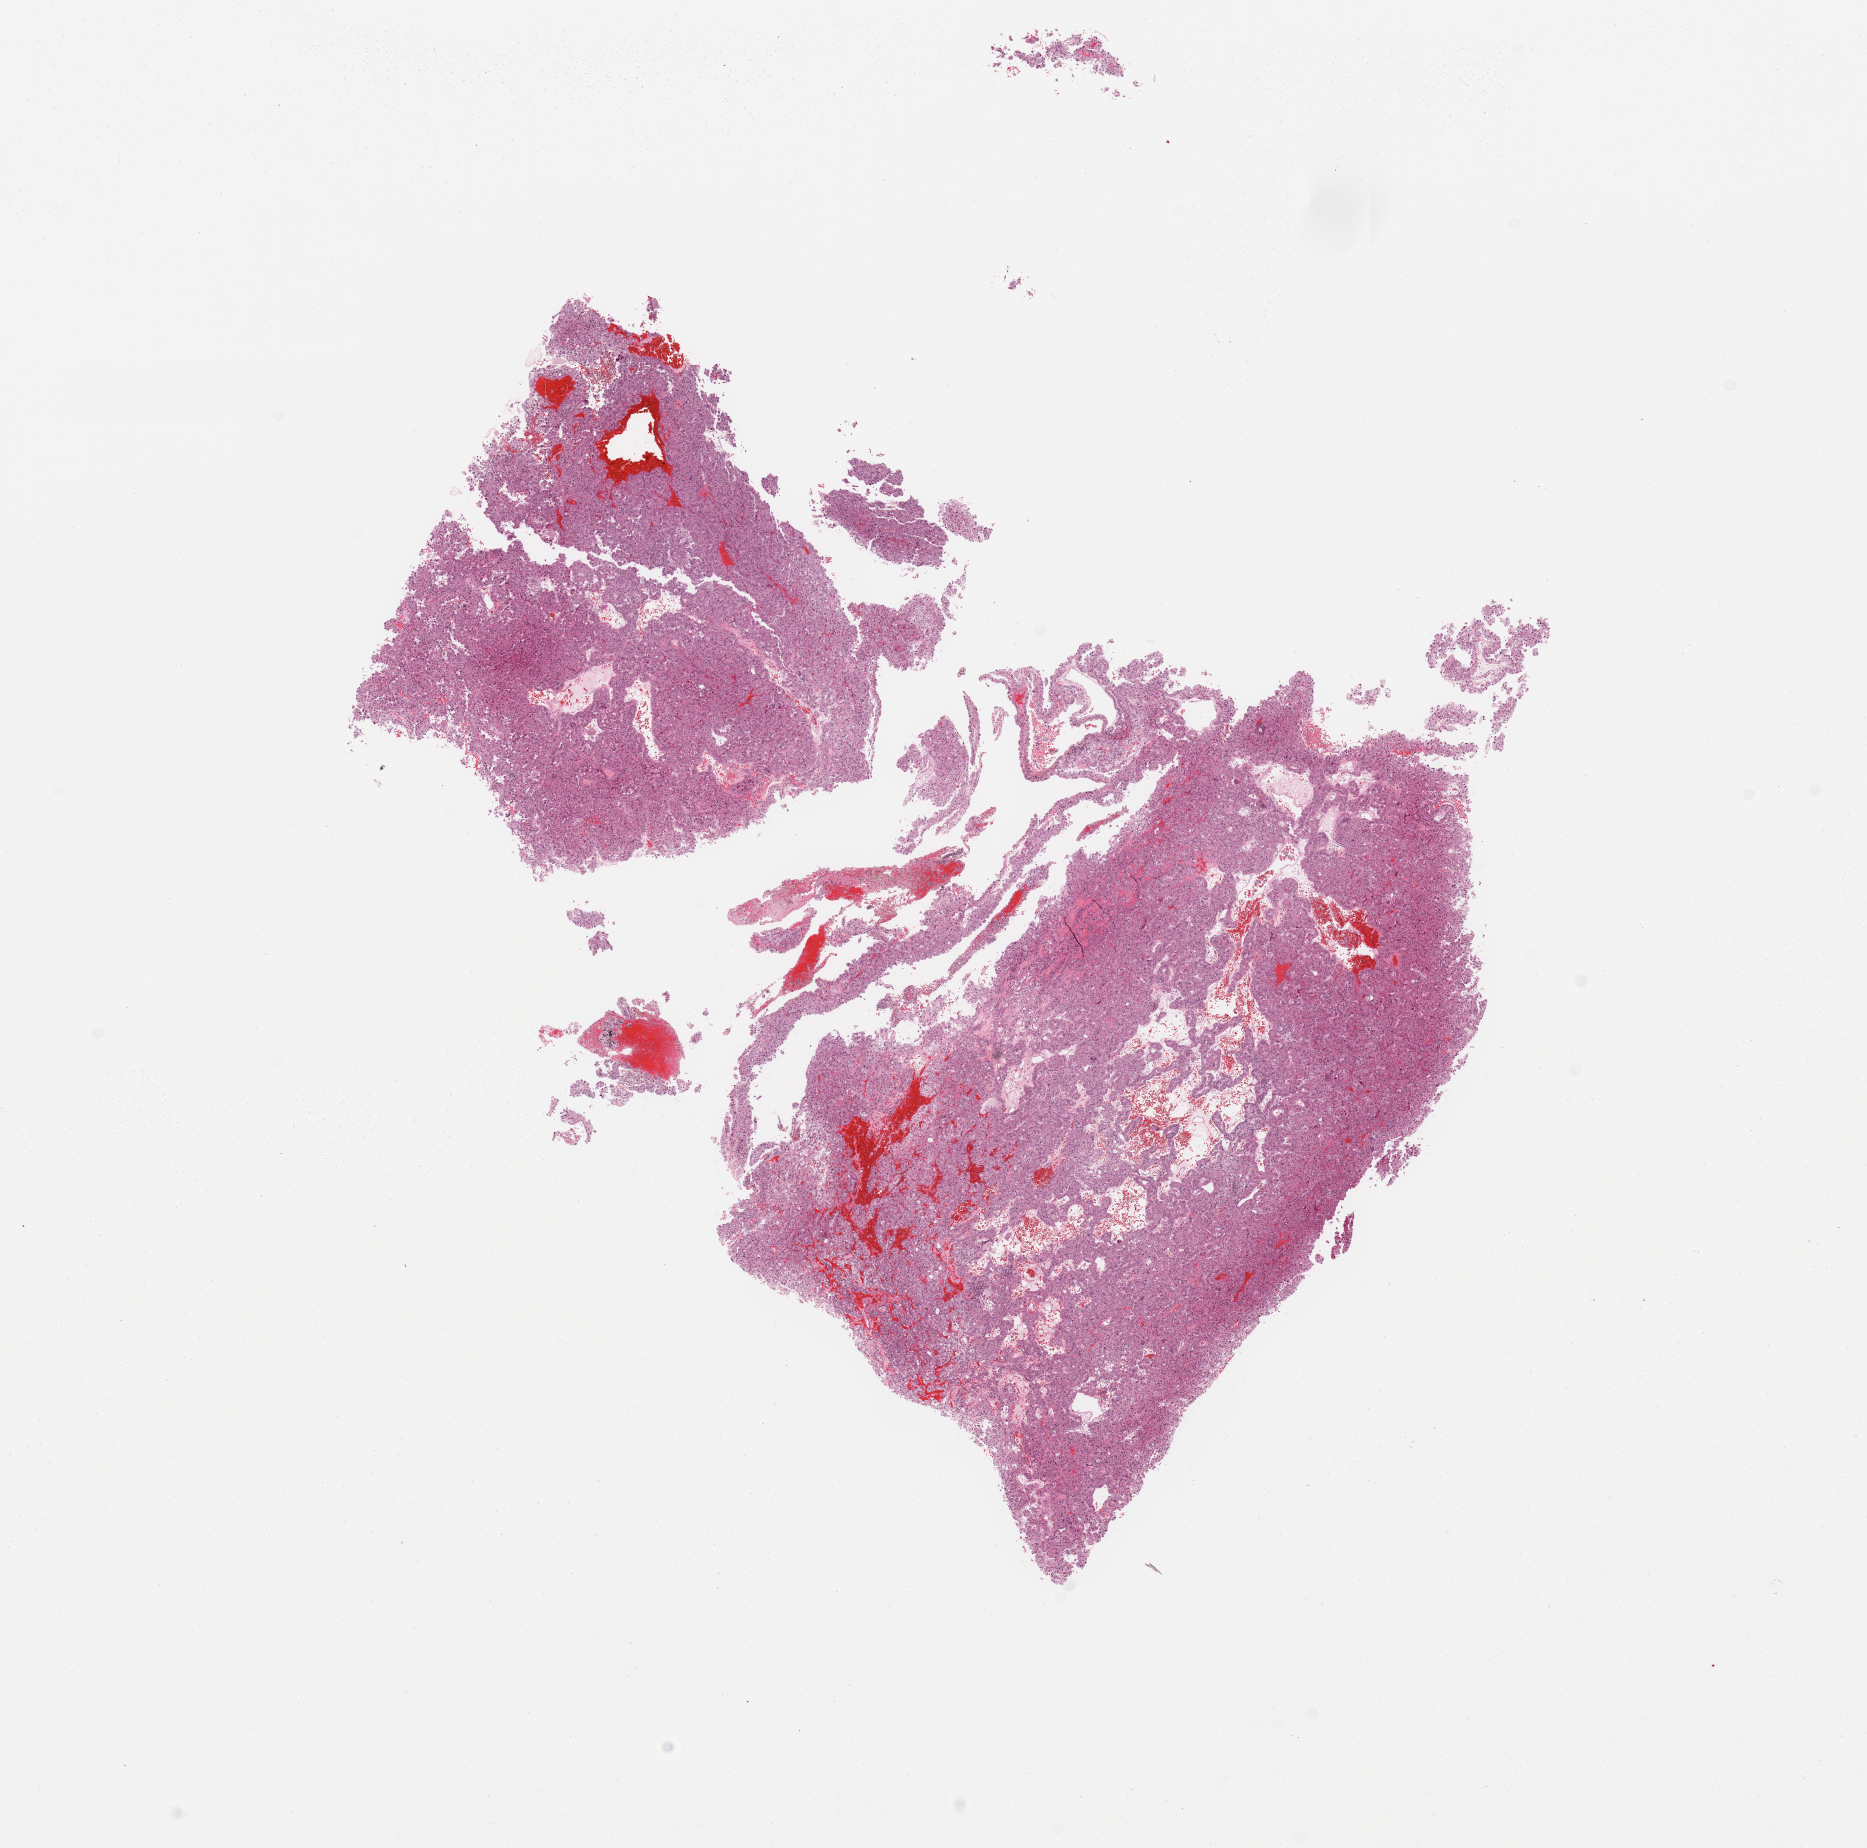
Digitized H&E-stained tissue section (whole slide), a low-resolution overview of the entire scanned area, about 14.8 x 14.6 mm (from a 20x scan), kidney, tumour tissue. Patient: female, age 68 years. Histologic grade: G4 (undifferentiated).
AJCC pathologic stage: I. Diagnosis: Renal cell carcinoma, NOS. Primary tumour site (as recorded): middle.